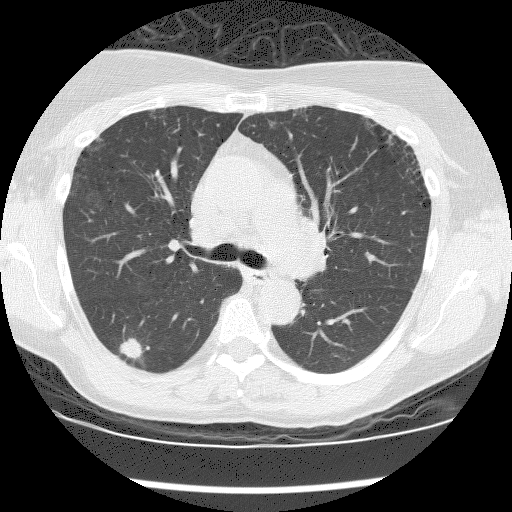
Low-dose screening chest CT, one axial slice; slice 119 of 176 in the series (ordered by position); lung window (W 1500 / L -600 HU); 512 × 512 image matrix.
Annotated regions visible in this slice (manually delineated by an expert):
- lesion 1 (tumor, lower lobe of right lung): box from (x=119, y=338) to (x=143, y=361) px